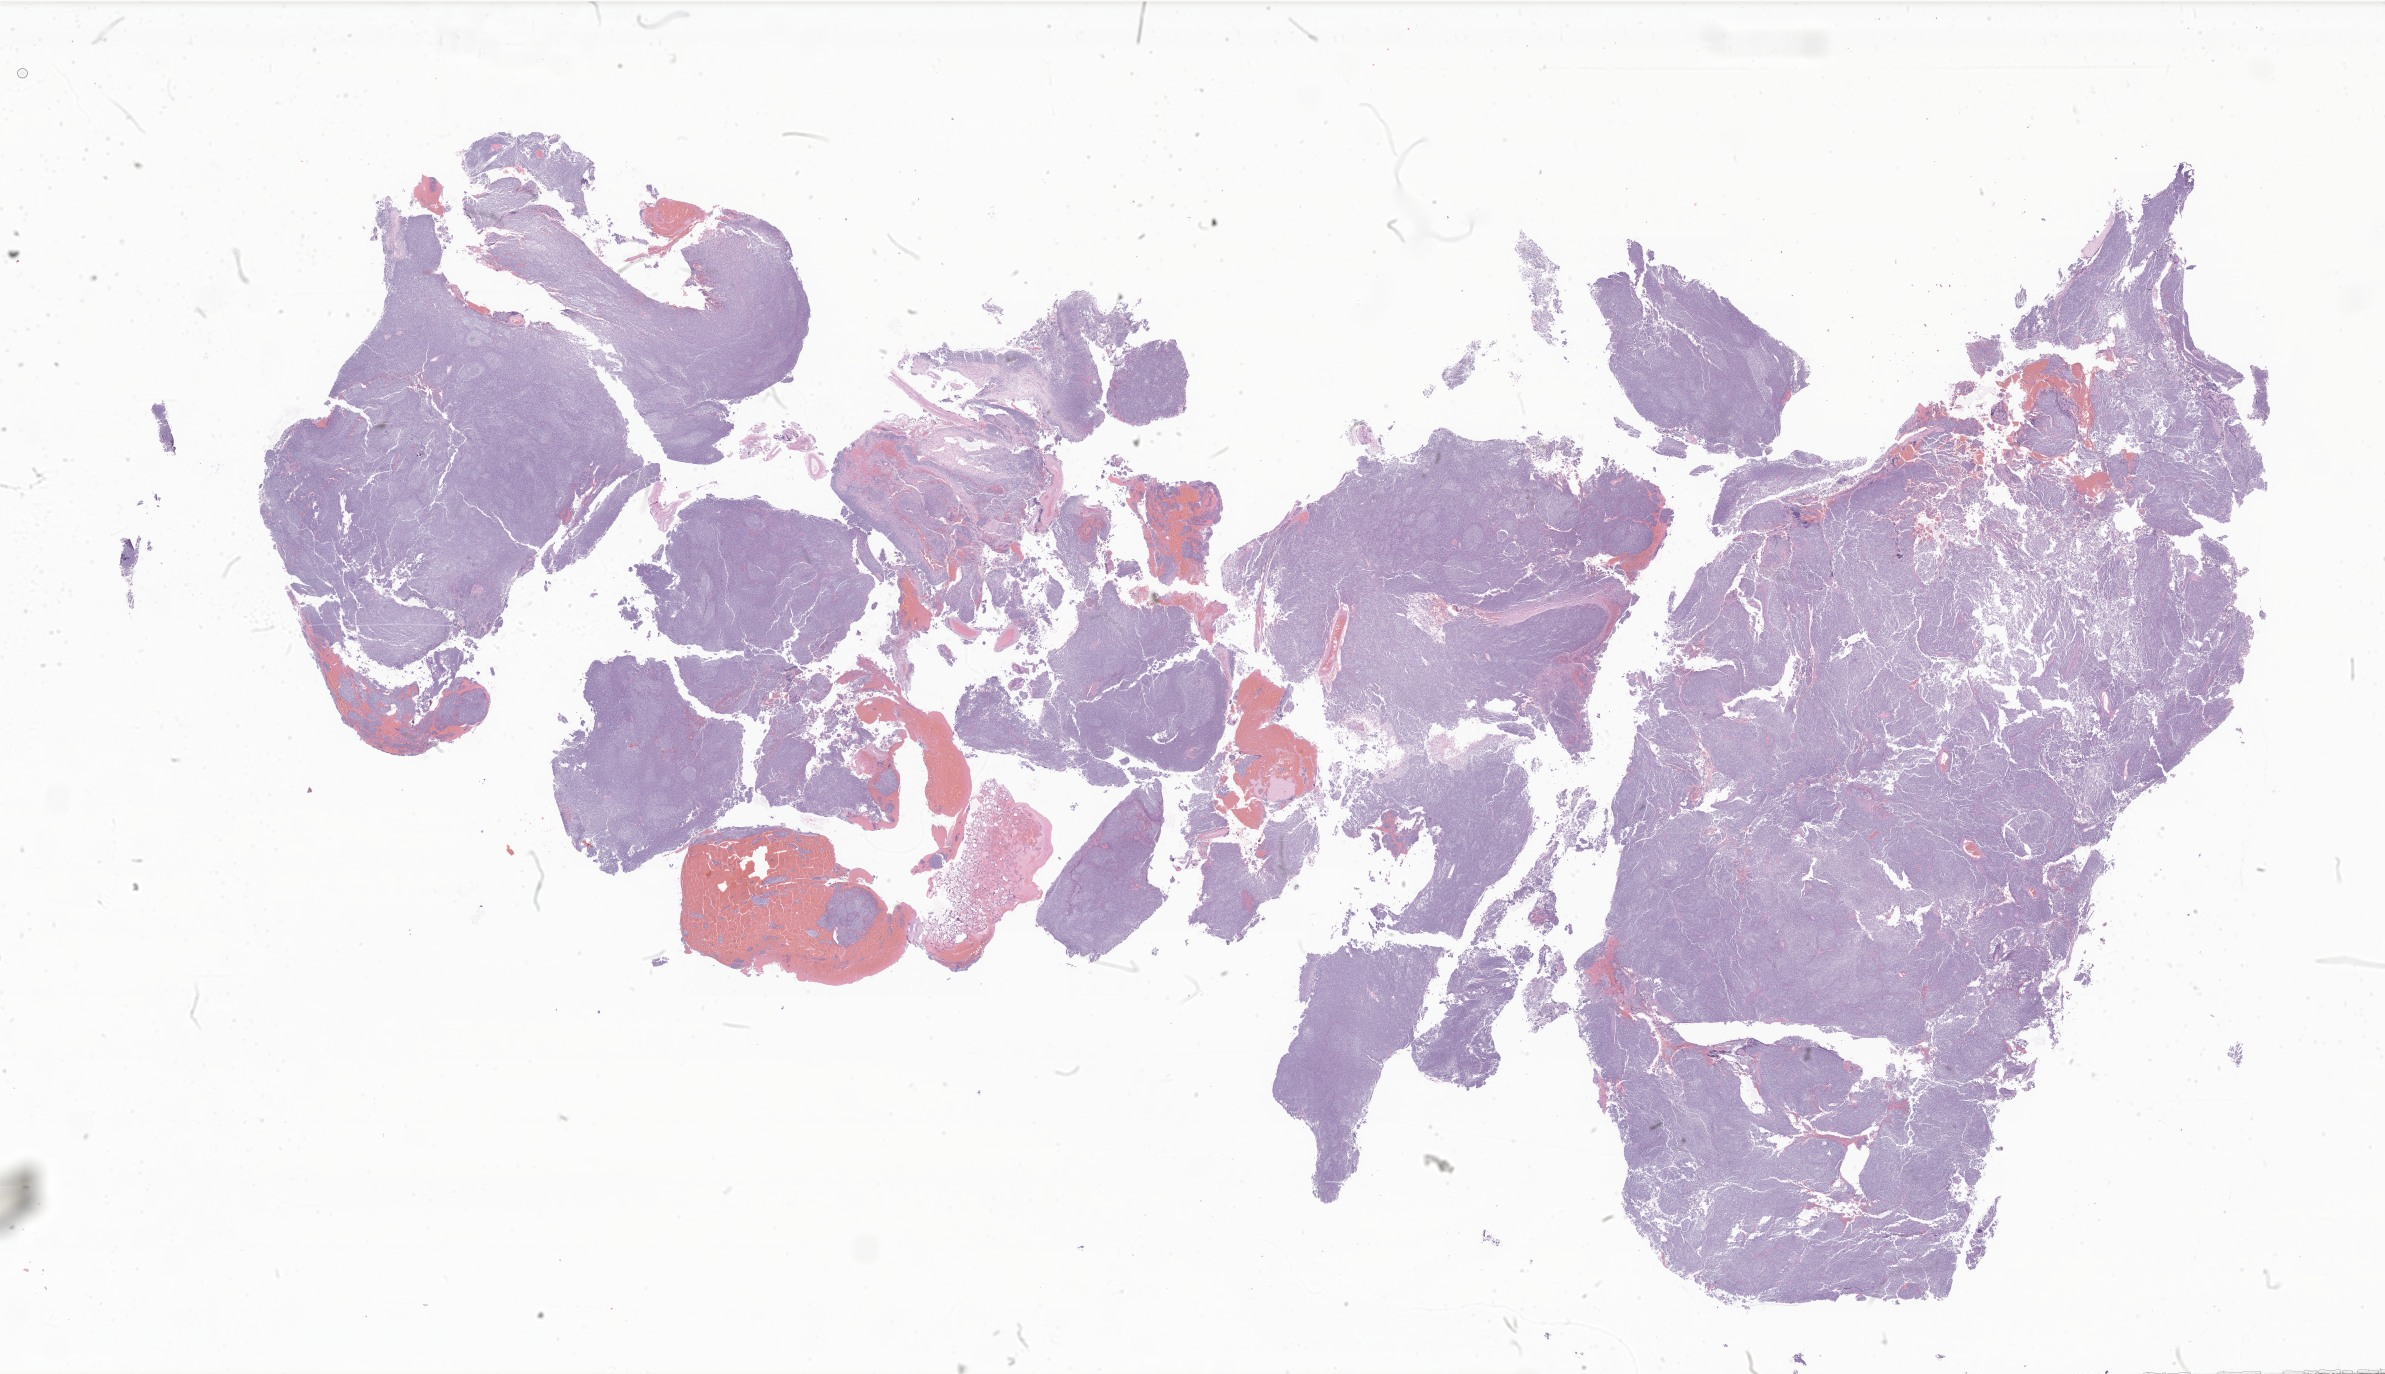
Whole-slide image, H&E stain of tumor tissue from the brain, a low-resolution overview of the entire scanned area, about 40.2 x 23.2 mm, formalin-fixed, paraffin-embedded (FFPE) tissue. Male patient, age 72 months.
* diagnosis (ICD-O-3 morphology term): Medulloblastoma, NOS